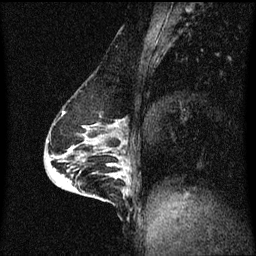
Breast MRI (dynamic contrast-enhanced), one sagittal slice; slice 30 of 60 in the series (ordered by position); dynamic contrast-enhanced series, image 2 of 3 at this slice position (ordered by acquisition); 1.5 T; TE 4.2 ms, TR 8.4 ms; 2 mm slice thickness; 256 × 256 image matrix, field of view 200 × 200 mm. Patient: female, 64 years.
Outlined on this slice (semi-automatically segmented with operator editing):
- analysis volume of interest (the breast-tissue region the enhancement analysis was run in; not a lesion): bounding box [x1, y1, x2, y2] px = [90, 164, 129, 203]
- tumour enhancement mask (voxels above the 70 % enhancement threshold inside the analysis volume of interest): [108, 164, 129, 193]